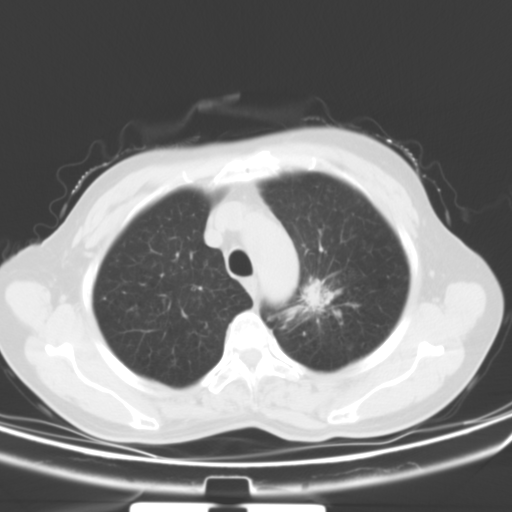
Chest CT, one axial slice; slice 45 of 53 in the series (ordered by position); 120 kVp; lung window (W 1500 / L -600 HU); 5 mm slice thickness; 512 × 512 image matrix, field of view 329 × 329 mm. Female patient, age 60 years. Case-level facts recorded for this patient, not image findings: clinical TNM (as recorded): T1b N0 M0.
Structures marked on this image (bounding box drawn by a radiologist):
- lung tumour (recorded histology: squamous cell carcinoma): bounding box (x1, y1, x2, y2) in pixels: (300, 274, 328, 316)